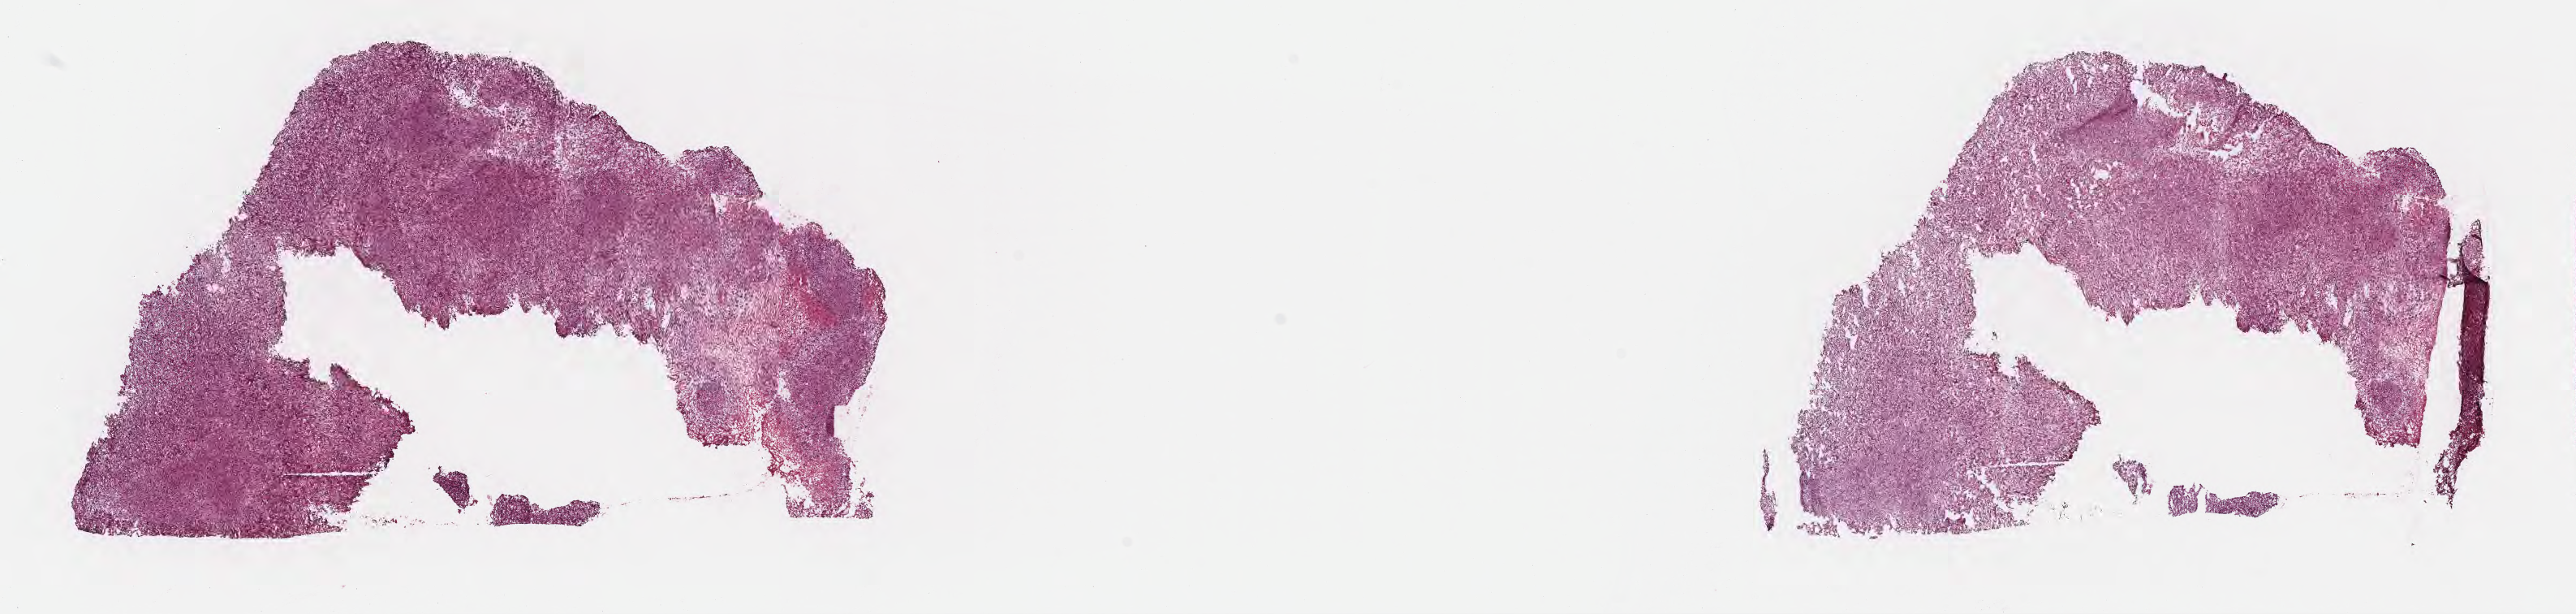
Whole-slide image, H&E stain, whole scanned area (about 25.7 x 6.1 mm) shown as a low-resolution overview. Frozen section (tissue freezing medium). Specimen: metastatic tumor tissue, resected from brain. Male, age 76 years at initial diagnosis. Slide review estimates, as recorded: tumor cells 80%, tumor nuclei 90%, stromal cells 15%, necrosis 5%, normal cells 0%. Inflammatory infiltration, as recorded: lymphocyte infiltration 0%, monocyte infiltration 0%, neutrophil infiltration 0%.
• patient diagnosis (primary): Spindle cell sarcoma